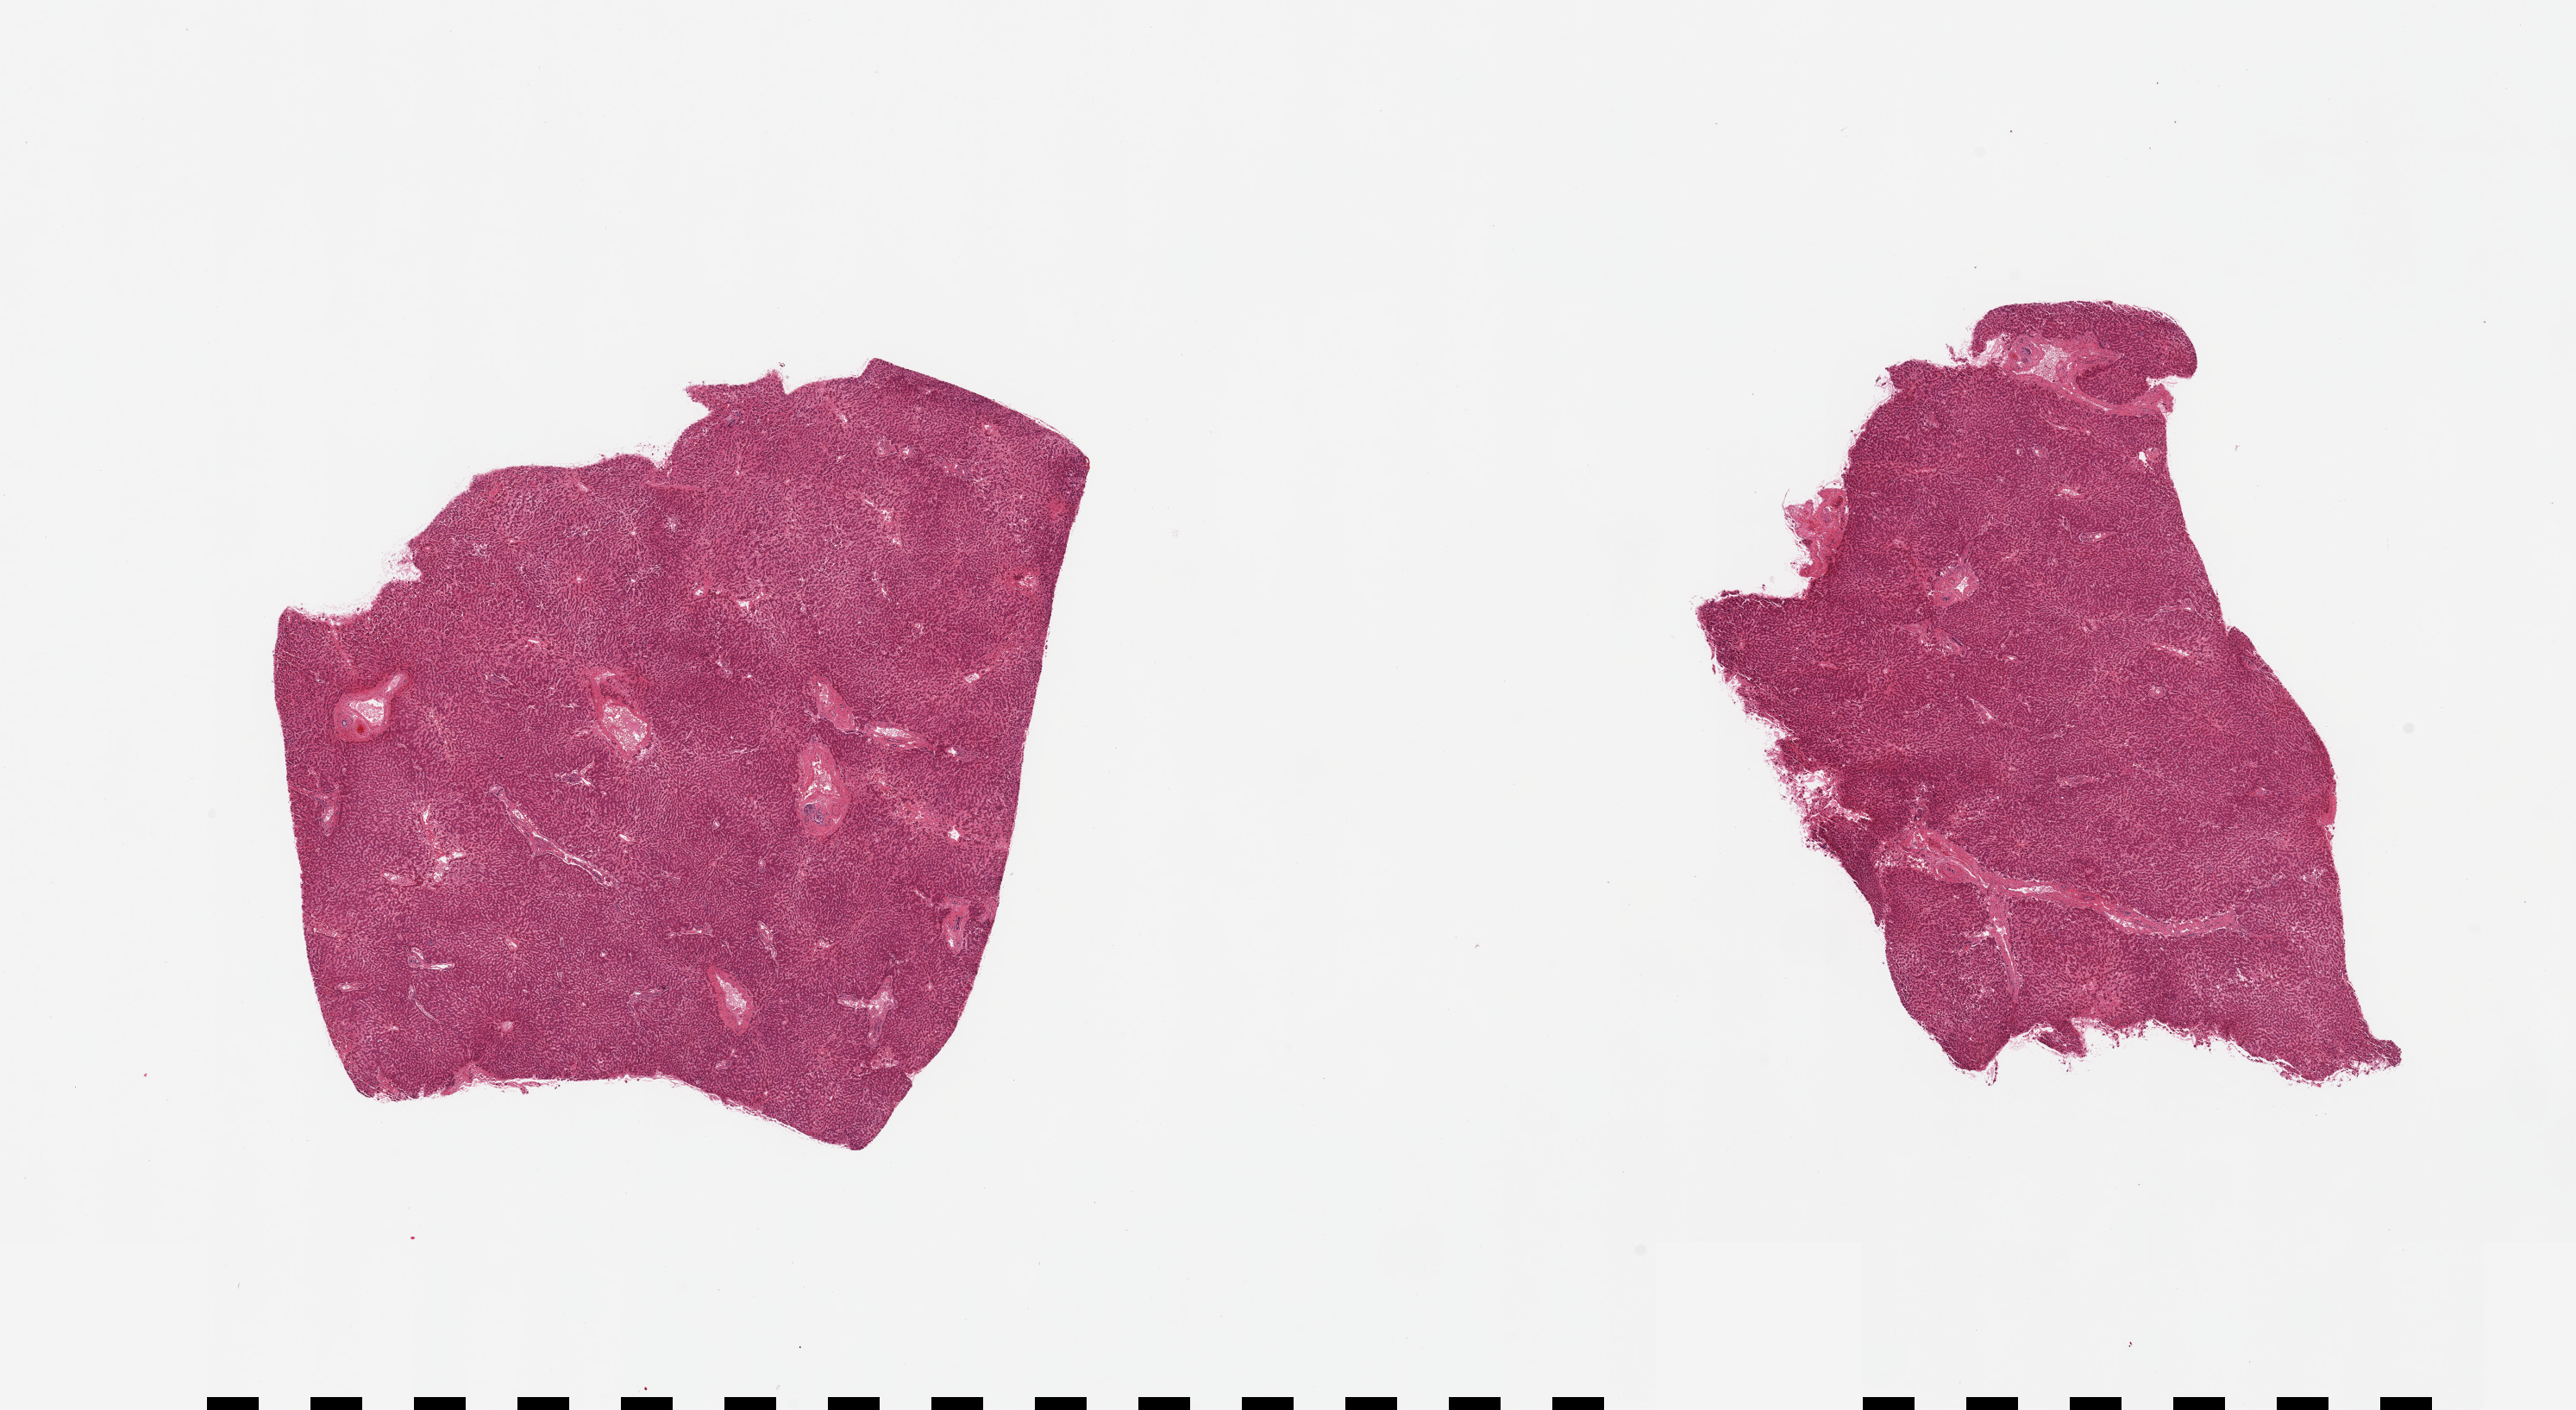
Digitized hematoxylin and eosin (H&E)-stained section, shown as a low-resolution overview of the whole scanned area (about 23.6 x 12.9 mm); PAXgene-fixed, paraffin-embedded tissue; sampled site (target tissue): liver; tissue donor sample. Male donor.
Review note (as recorded): 2 pieces.